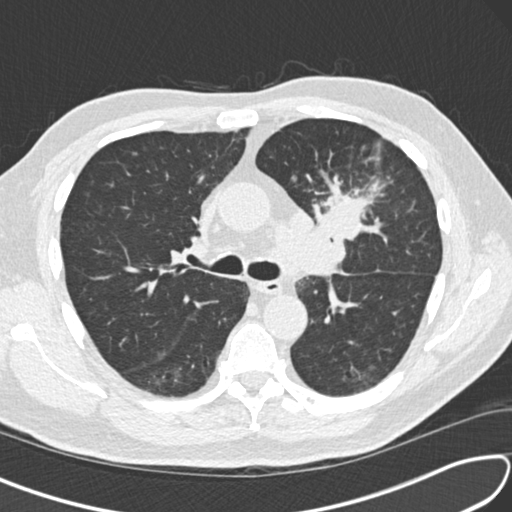
Low-dose screening chest CT, one axial slice; slice 99 of 156 in the series (ordered by position); reconstruction kernel B30f; lung window (W 1500 / L -600 HU); 2 mm slice thickness; 512 × 512 image matrix, field of view 340 × 340 mm.
Structures marked on this image (expert manual segmentation):
- lesion 1 (tumor, upper lobe of left lung): bounding box <319,195,363,240> (left, top, right, bottom; pixels)